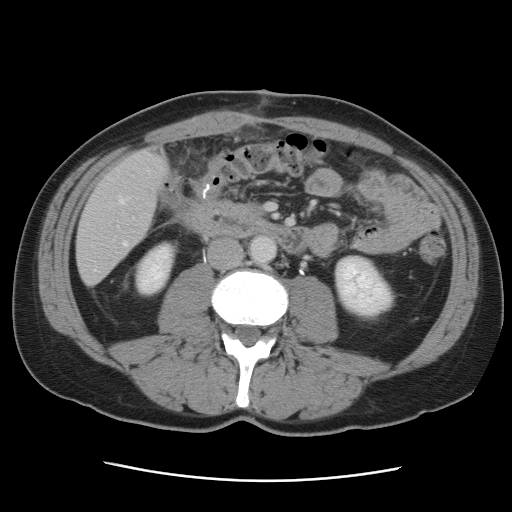
Contrast-enhanced abdominal CT, one axial slice. Intravenous contrast given. Soft-tissue window (W 400 / L 40 HU). 5 mm slice thickness. 512 × 512 image matrix. Male patient, age 59 years. From the clinical record (not read from this slice): diagnosis: colorectal cancer liver metastases, imaged before liver resection; multiple liver metastases: yes; largest metastasis: 0.6 cm; chemotherapy before resection: no.
Structures marked on this image (manually delineated by an expert):
- hepatic veins: bounding box (x1, y1, x2, y2) in pixels: (95, 170, 149, 271)
- liver: (78, 149, 168, 284)
- planned liver remnant (the part of the liver to remain after resection): (78, 148, 168, 254)